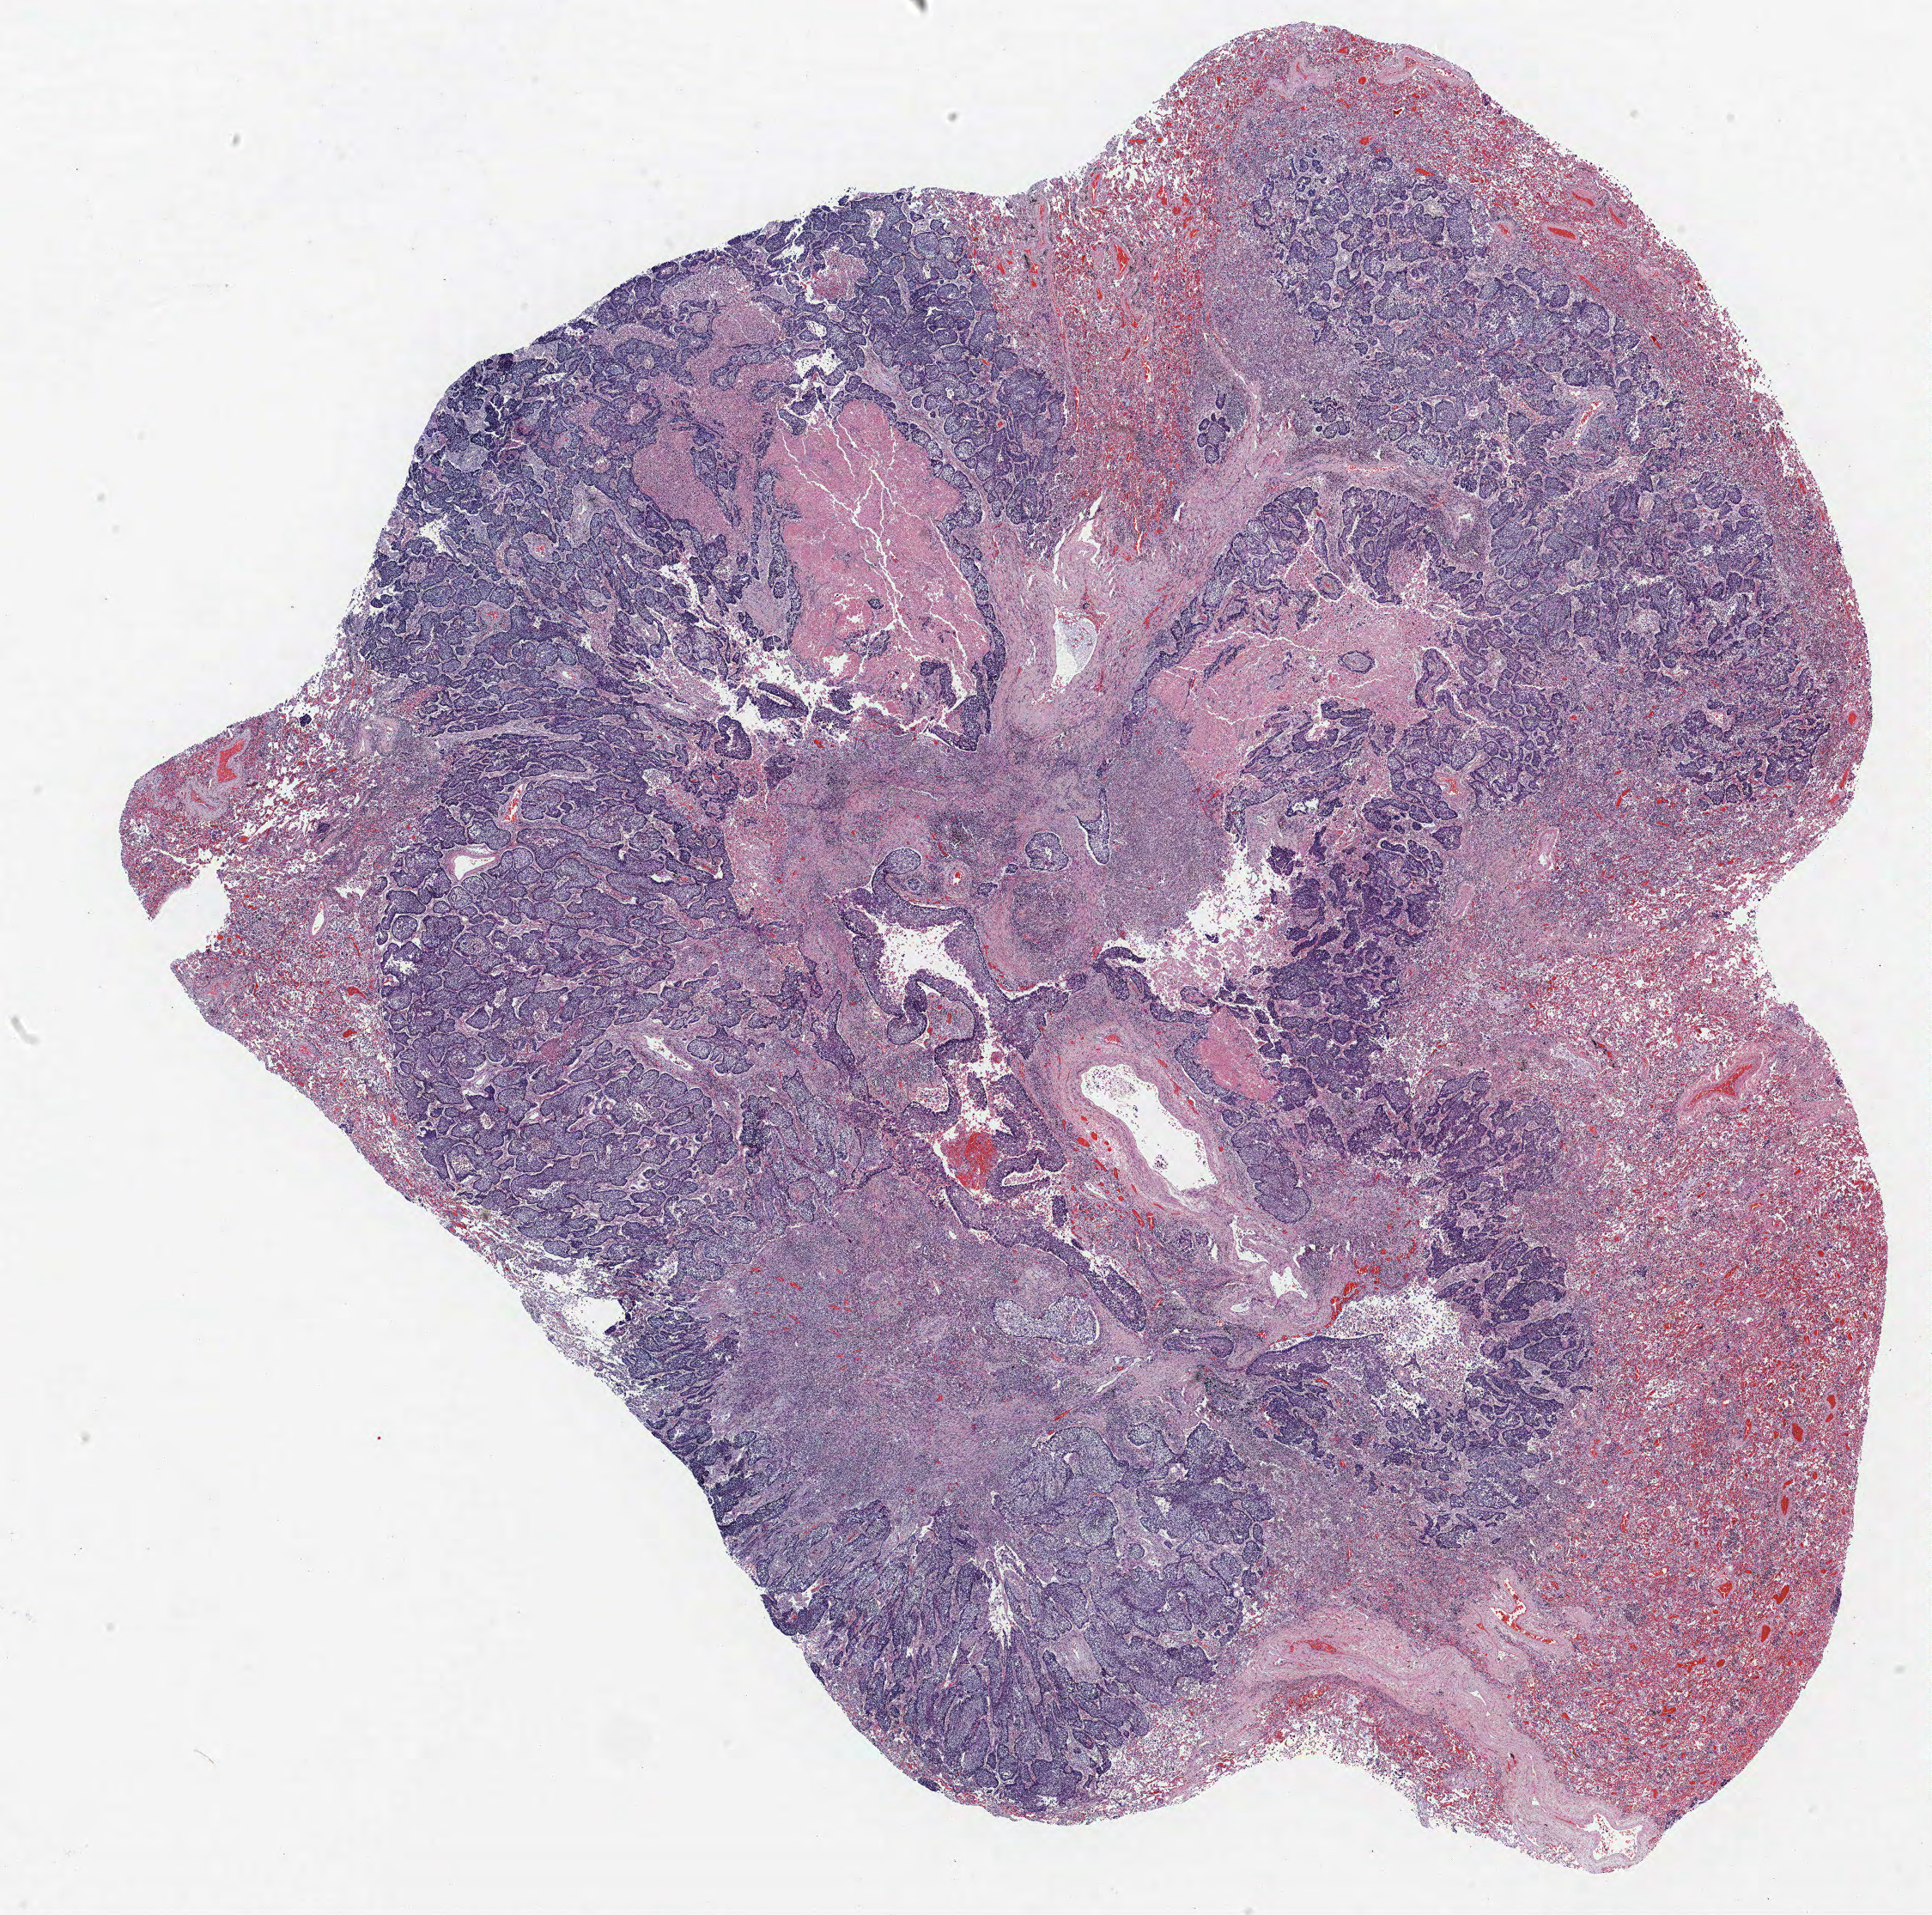
Whole-slide histology image, H&E-stained, whole scanned area (about 18.0 x 17.8 mm, from a 40x scan) shown as a low-resolution overview. FFPE section. Lung. Female patient, aged 61 at enrolment. Grade: well differentiated (G1).
ICD-O-3 topography: upper lobe of lung (C34.1). Stage (AJCC 6th edition): IIIB. Tumour size (pathology): 30 mm. Participant's lung-cancer diagnosis: Adenocarcinoma, NOS (ICD-O-3 8140/3). Primary tumour location (clinical record): right upper lobe. Note: participant had 2 primary lung cancers recorded; fields above describe the first.